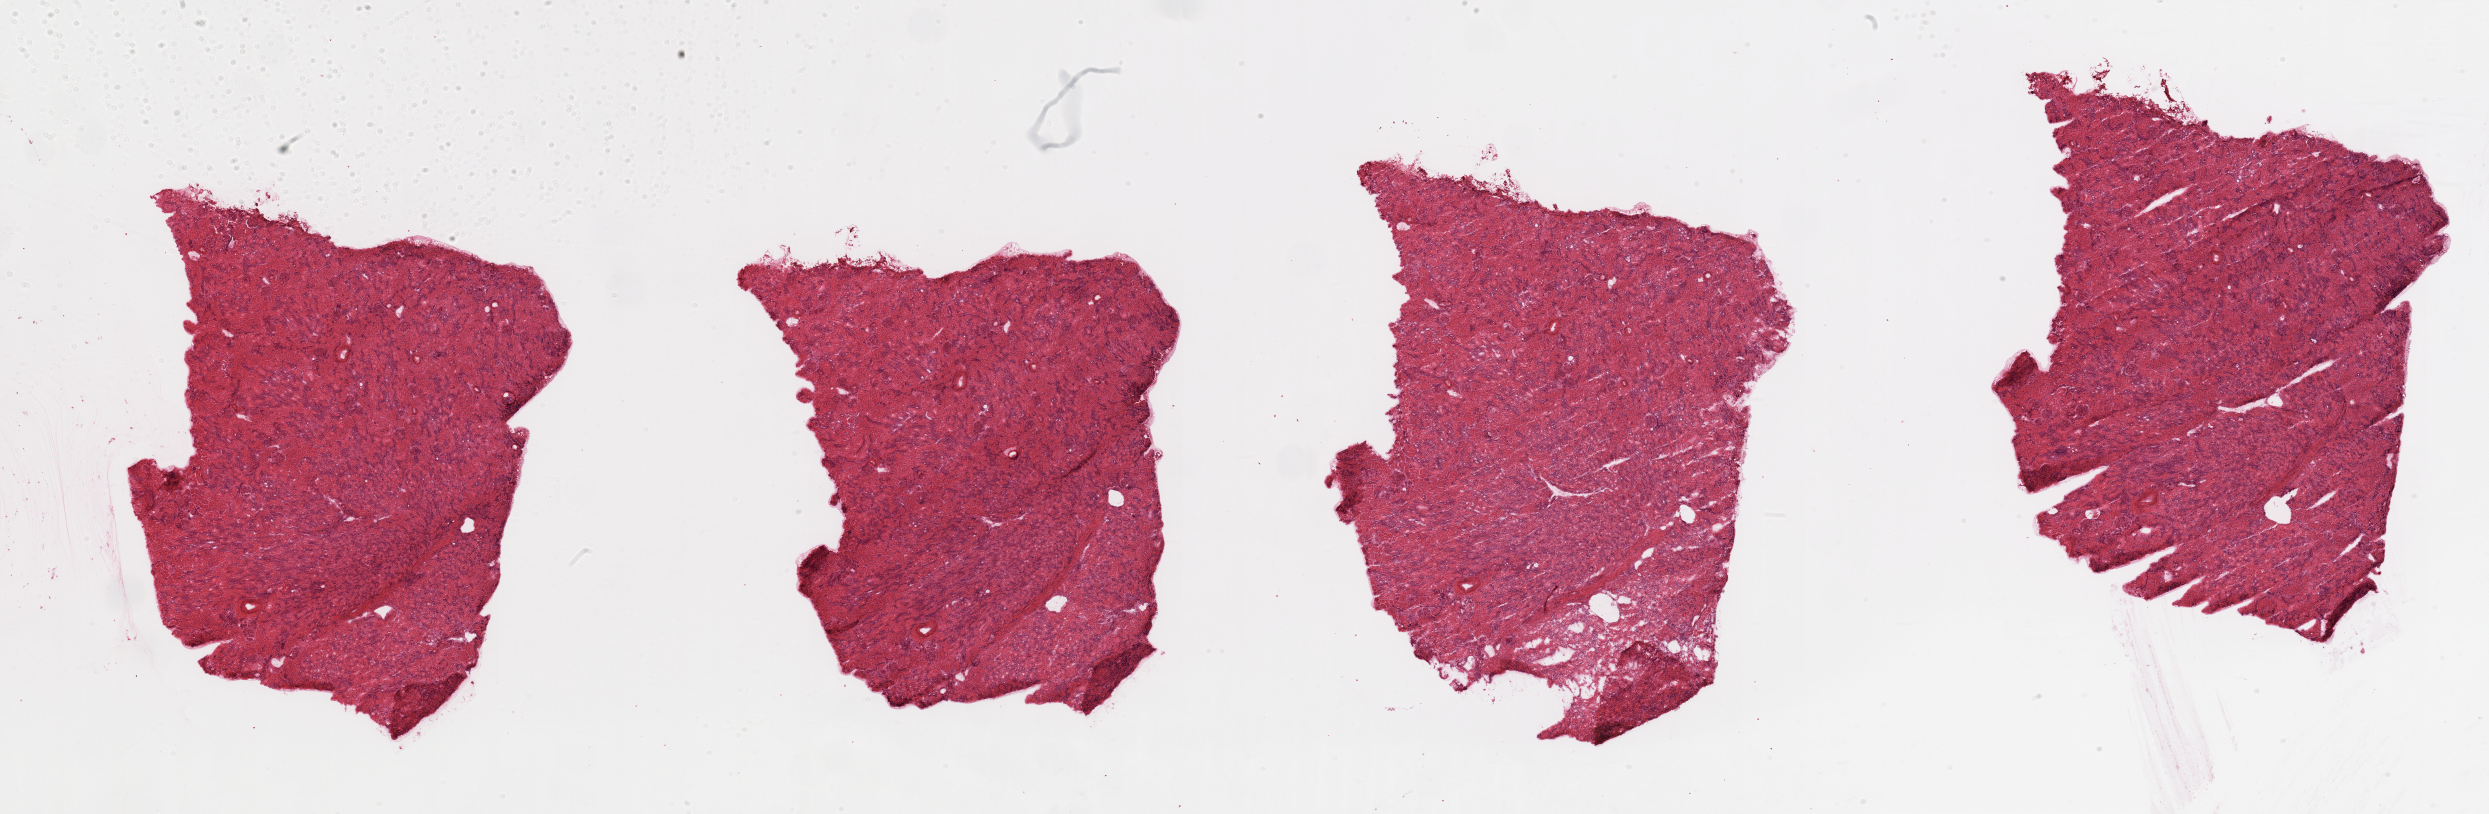
Whole-slide histology image, Hematoxylin and eosin (H&E) stained, whole scanned area (about 39.4 x 12.9 mm, slide scanned at 20x) shown as a low-resolution overview; normal (non-tumour) tissue sample, kidney. Patient: male, age 54 years.
* this section: normal (non-tumour) tissue from the same patient
* patient diagnosis: Renal cell carcinoma, NOS